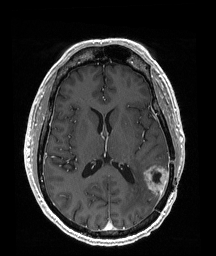
Brain MRI from a brain-tumour surgery series, one axial slice; slice 87 of 192 in the series (ordered by position); T1-weighted post-contrast; 1 mm slice thickness; 216 × 256 image matrix. From the clinical record (not read from this slice): histopathology: Glioblastoma; WHO grade: 4; IDH mutation: no.
Annotated regions visible in this slice (outlined manually by an expert reader):
- tumour: bounding box (x1, y1, x2, y2) in pixels: (144, 166, 170, 197)